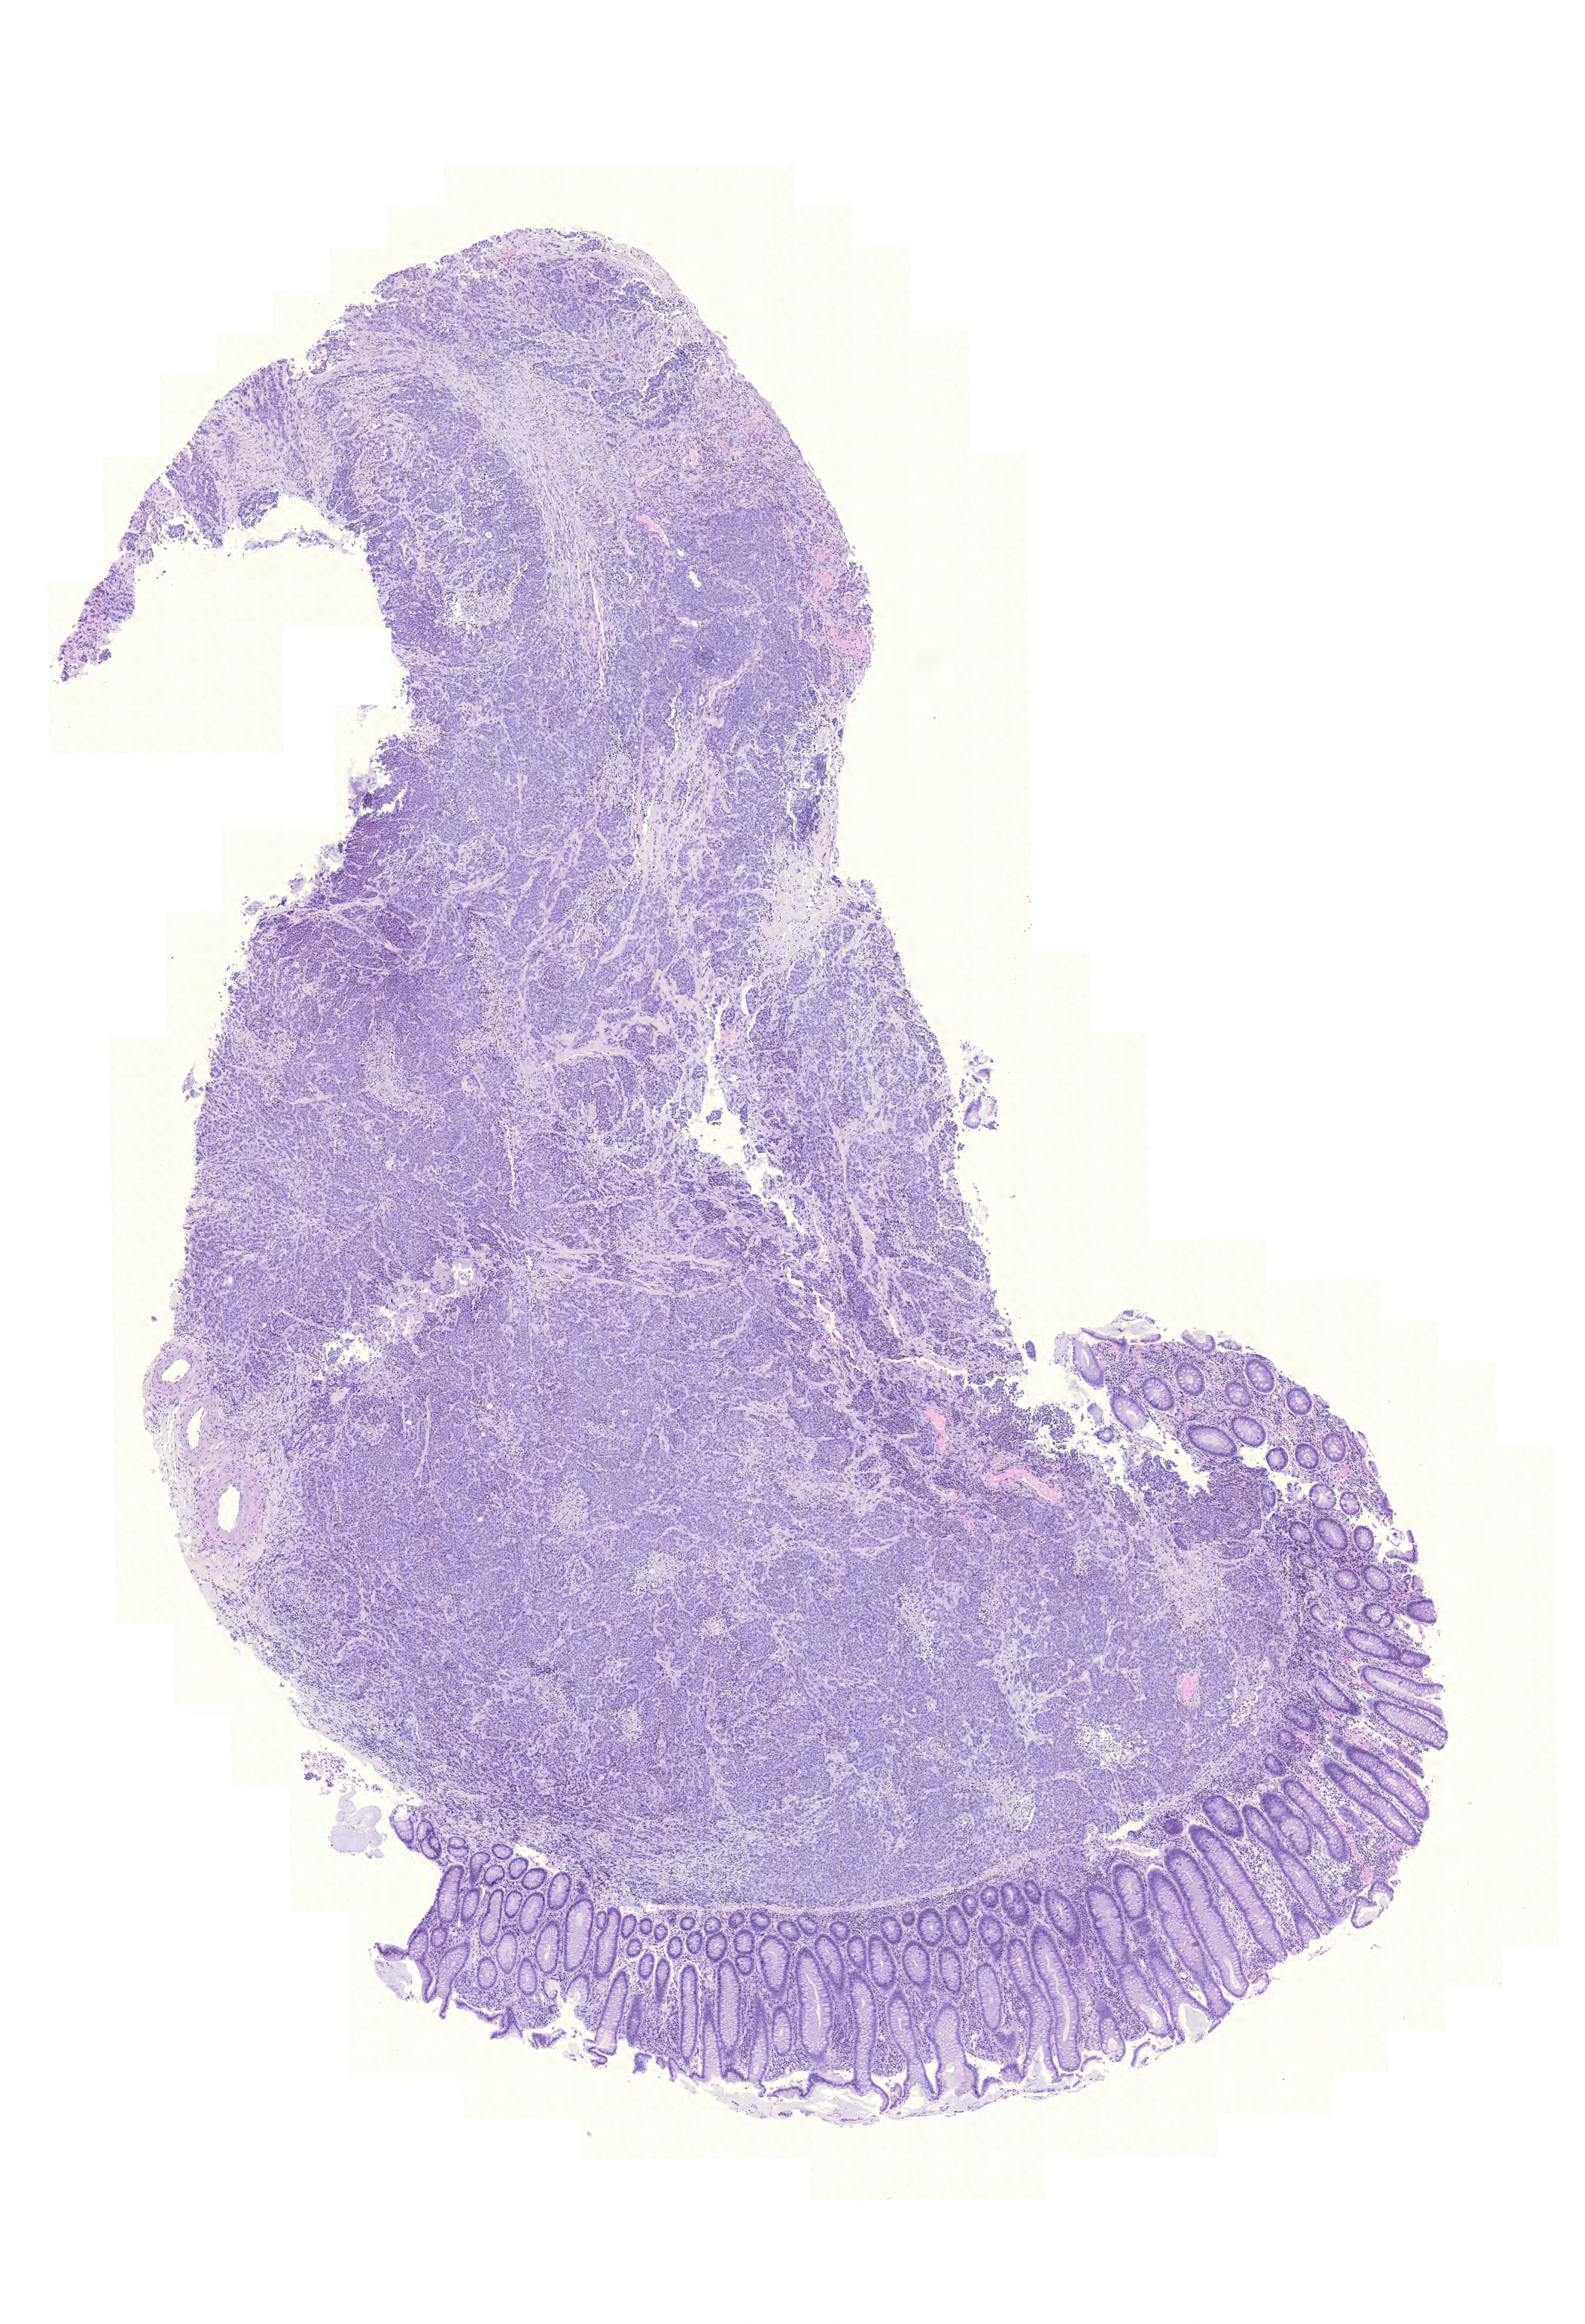
Hematoxylin and eosin (H&E) stained whole-slide image — shown as a low-resolution overview of the whole scanned area (about 7.9 x 11.6 mm, acquisition: 20x scan). FFPE section. Colon, primary tumour sample. Patient: female, age at initial diagnosis 86 years.
Histologic diagnosis: Adenocarcinoma, NOS (ascending colon).